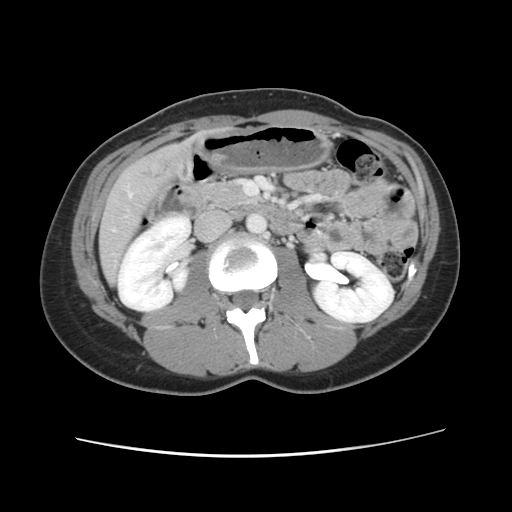
Contrast-enhanced abdominal CT, one axial slice; position 32 of 134 along the scan axis; 120 kVp; soft-tissue window (W 400 / L 40 HU); 2.5 mm slice thickness; 512 × 512 image matrix, field of view 339 × 339 mm. Female patient, age 33 years. From the clinical record (not read from this slice): diagnosis: colorectal cancer liver metastases, imaged before liver resection; multiple liver metastases: yes; largest metastasis: 4.5 cm; disease in both lobes: yes.
Outlined on this slice (manually delineated by an expert):
- hepatic veins: bounding box <129,193,132,196> (left, top, right, bottom; pixels)
- liver: <100,141,195,285>
- planned liver remnant (the part of the liver to remain after resection): <100,243,120,284>
- liver metastasis: <137,156,175,181>